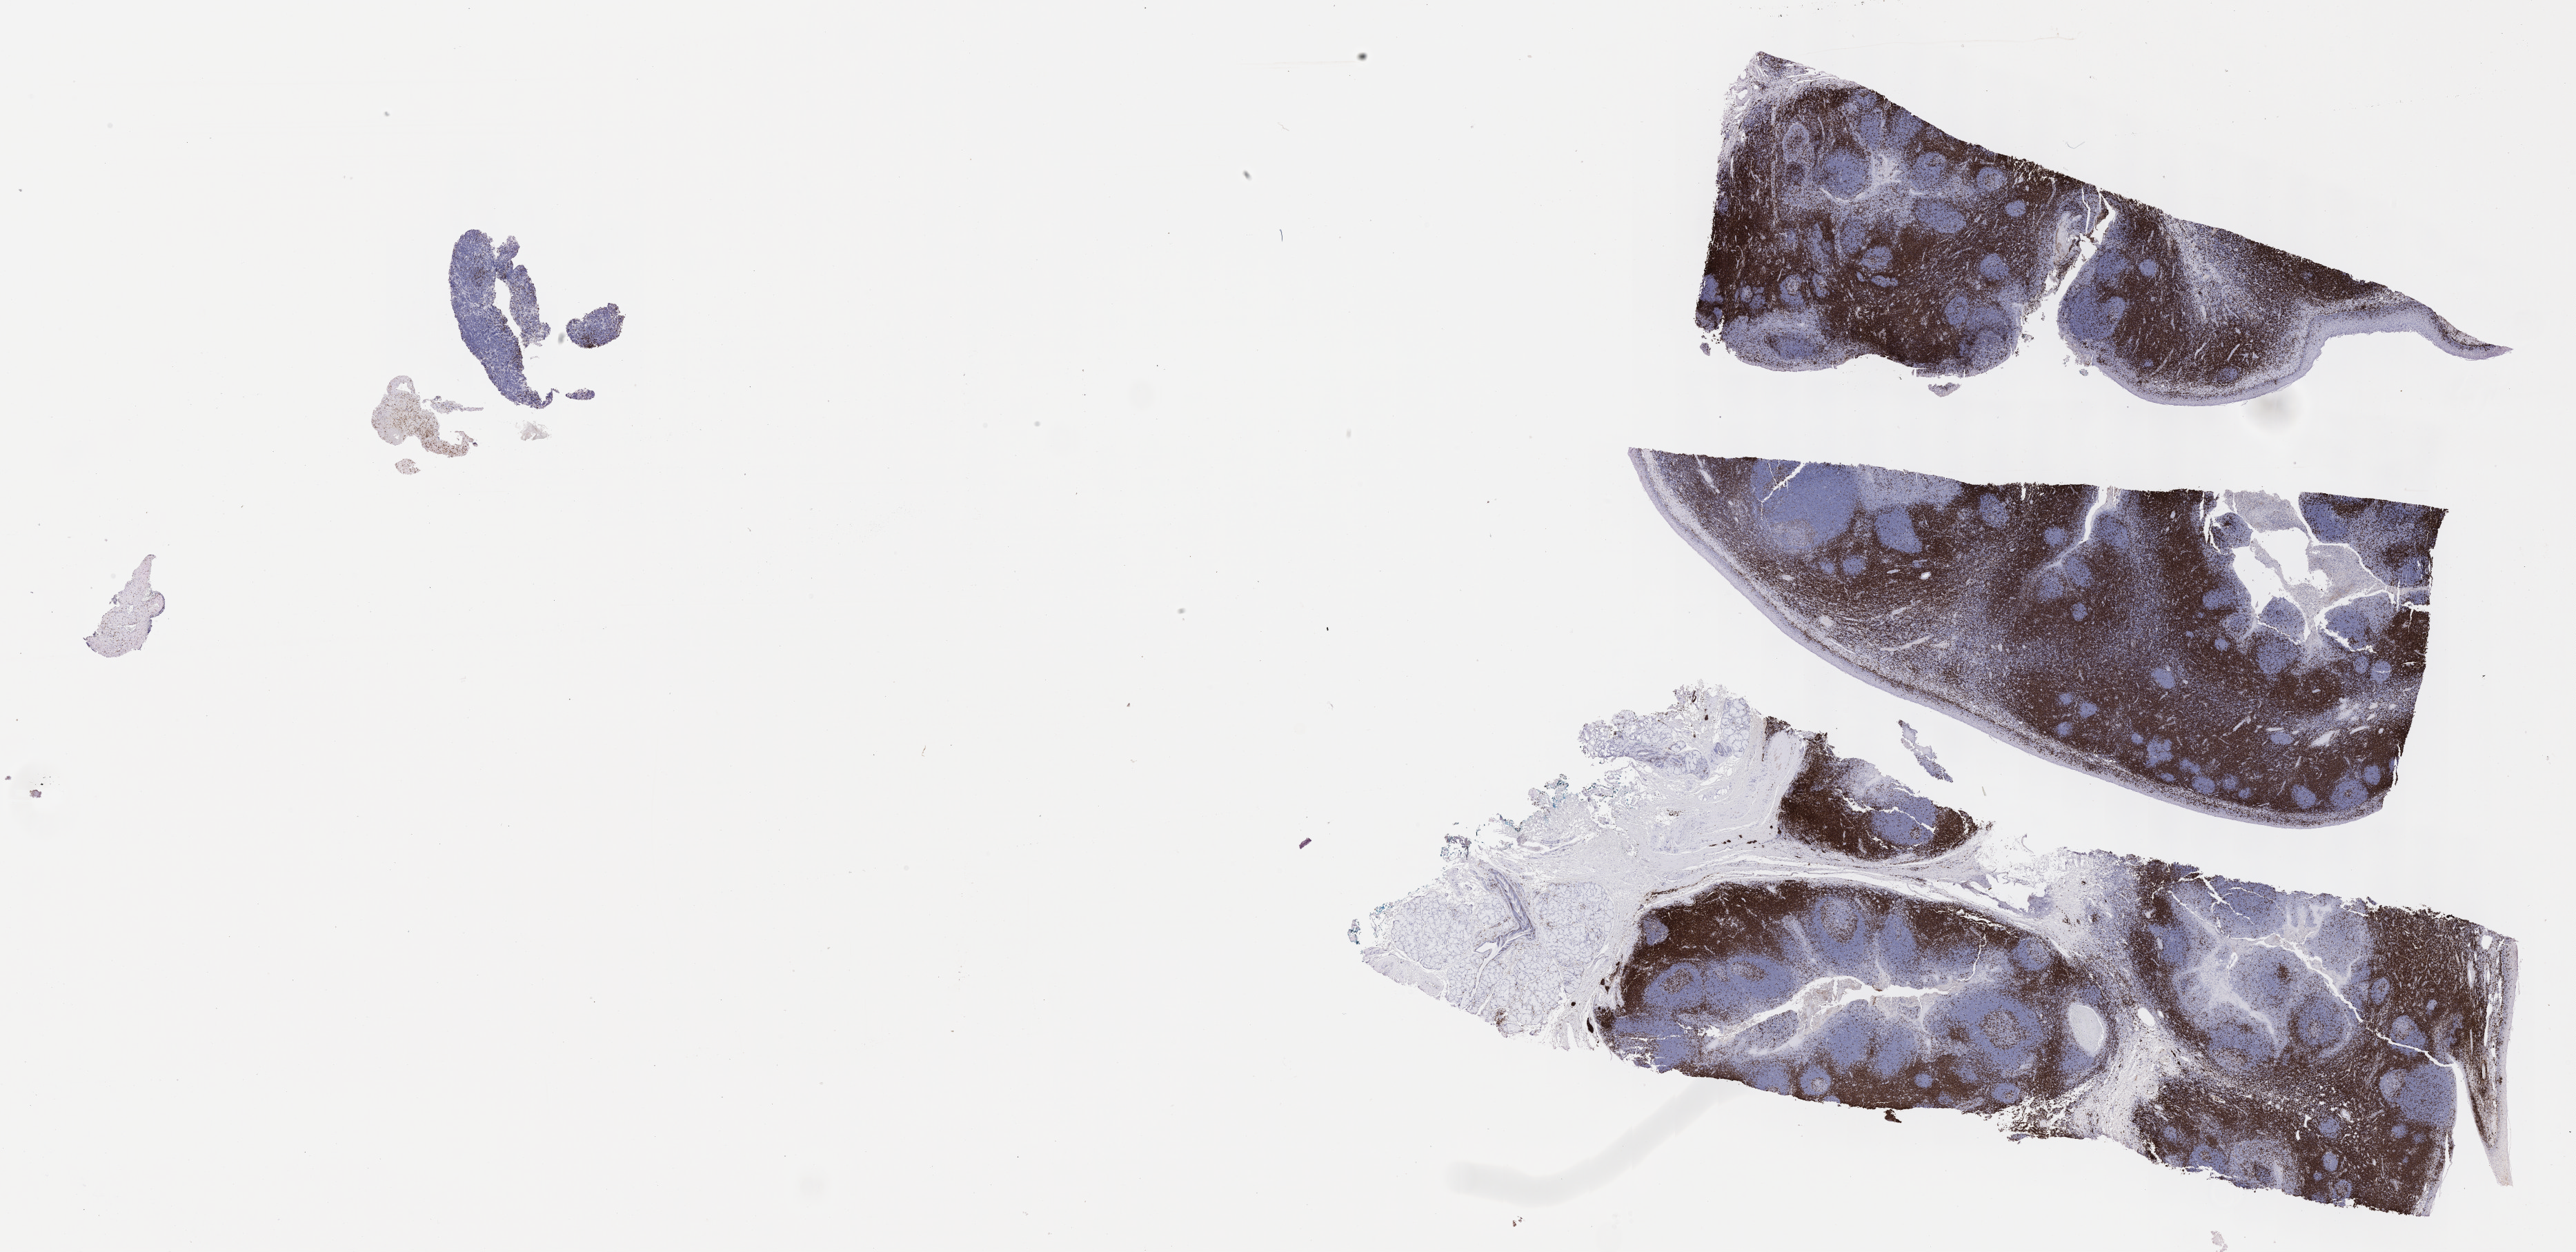
Immunohistochemistry (IHC) whole-slide image stained for CD3 — low-resolution overview of the scanned area, about 30.2 x 14.7 mm, tumor tissue, site: abdomen proper. Patient: female, age at initial diagnosis 7 years.
Diagnosis: Burkitt lymphoma, NOS.